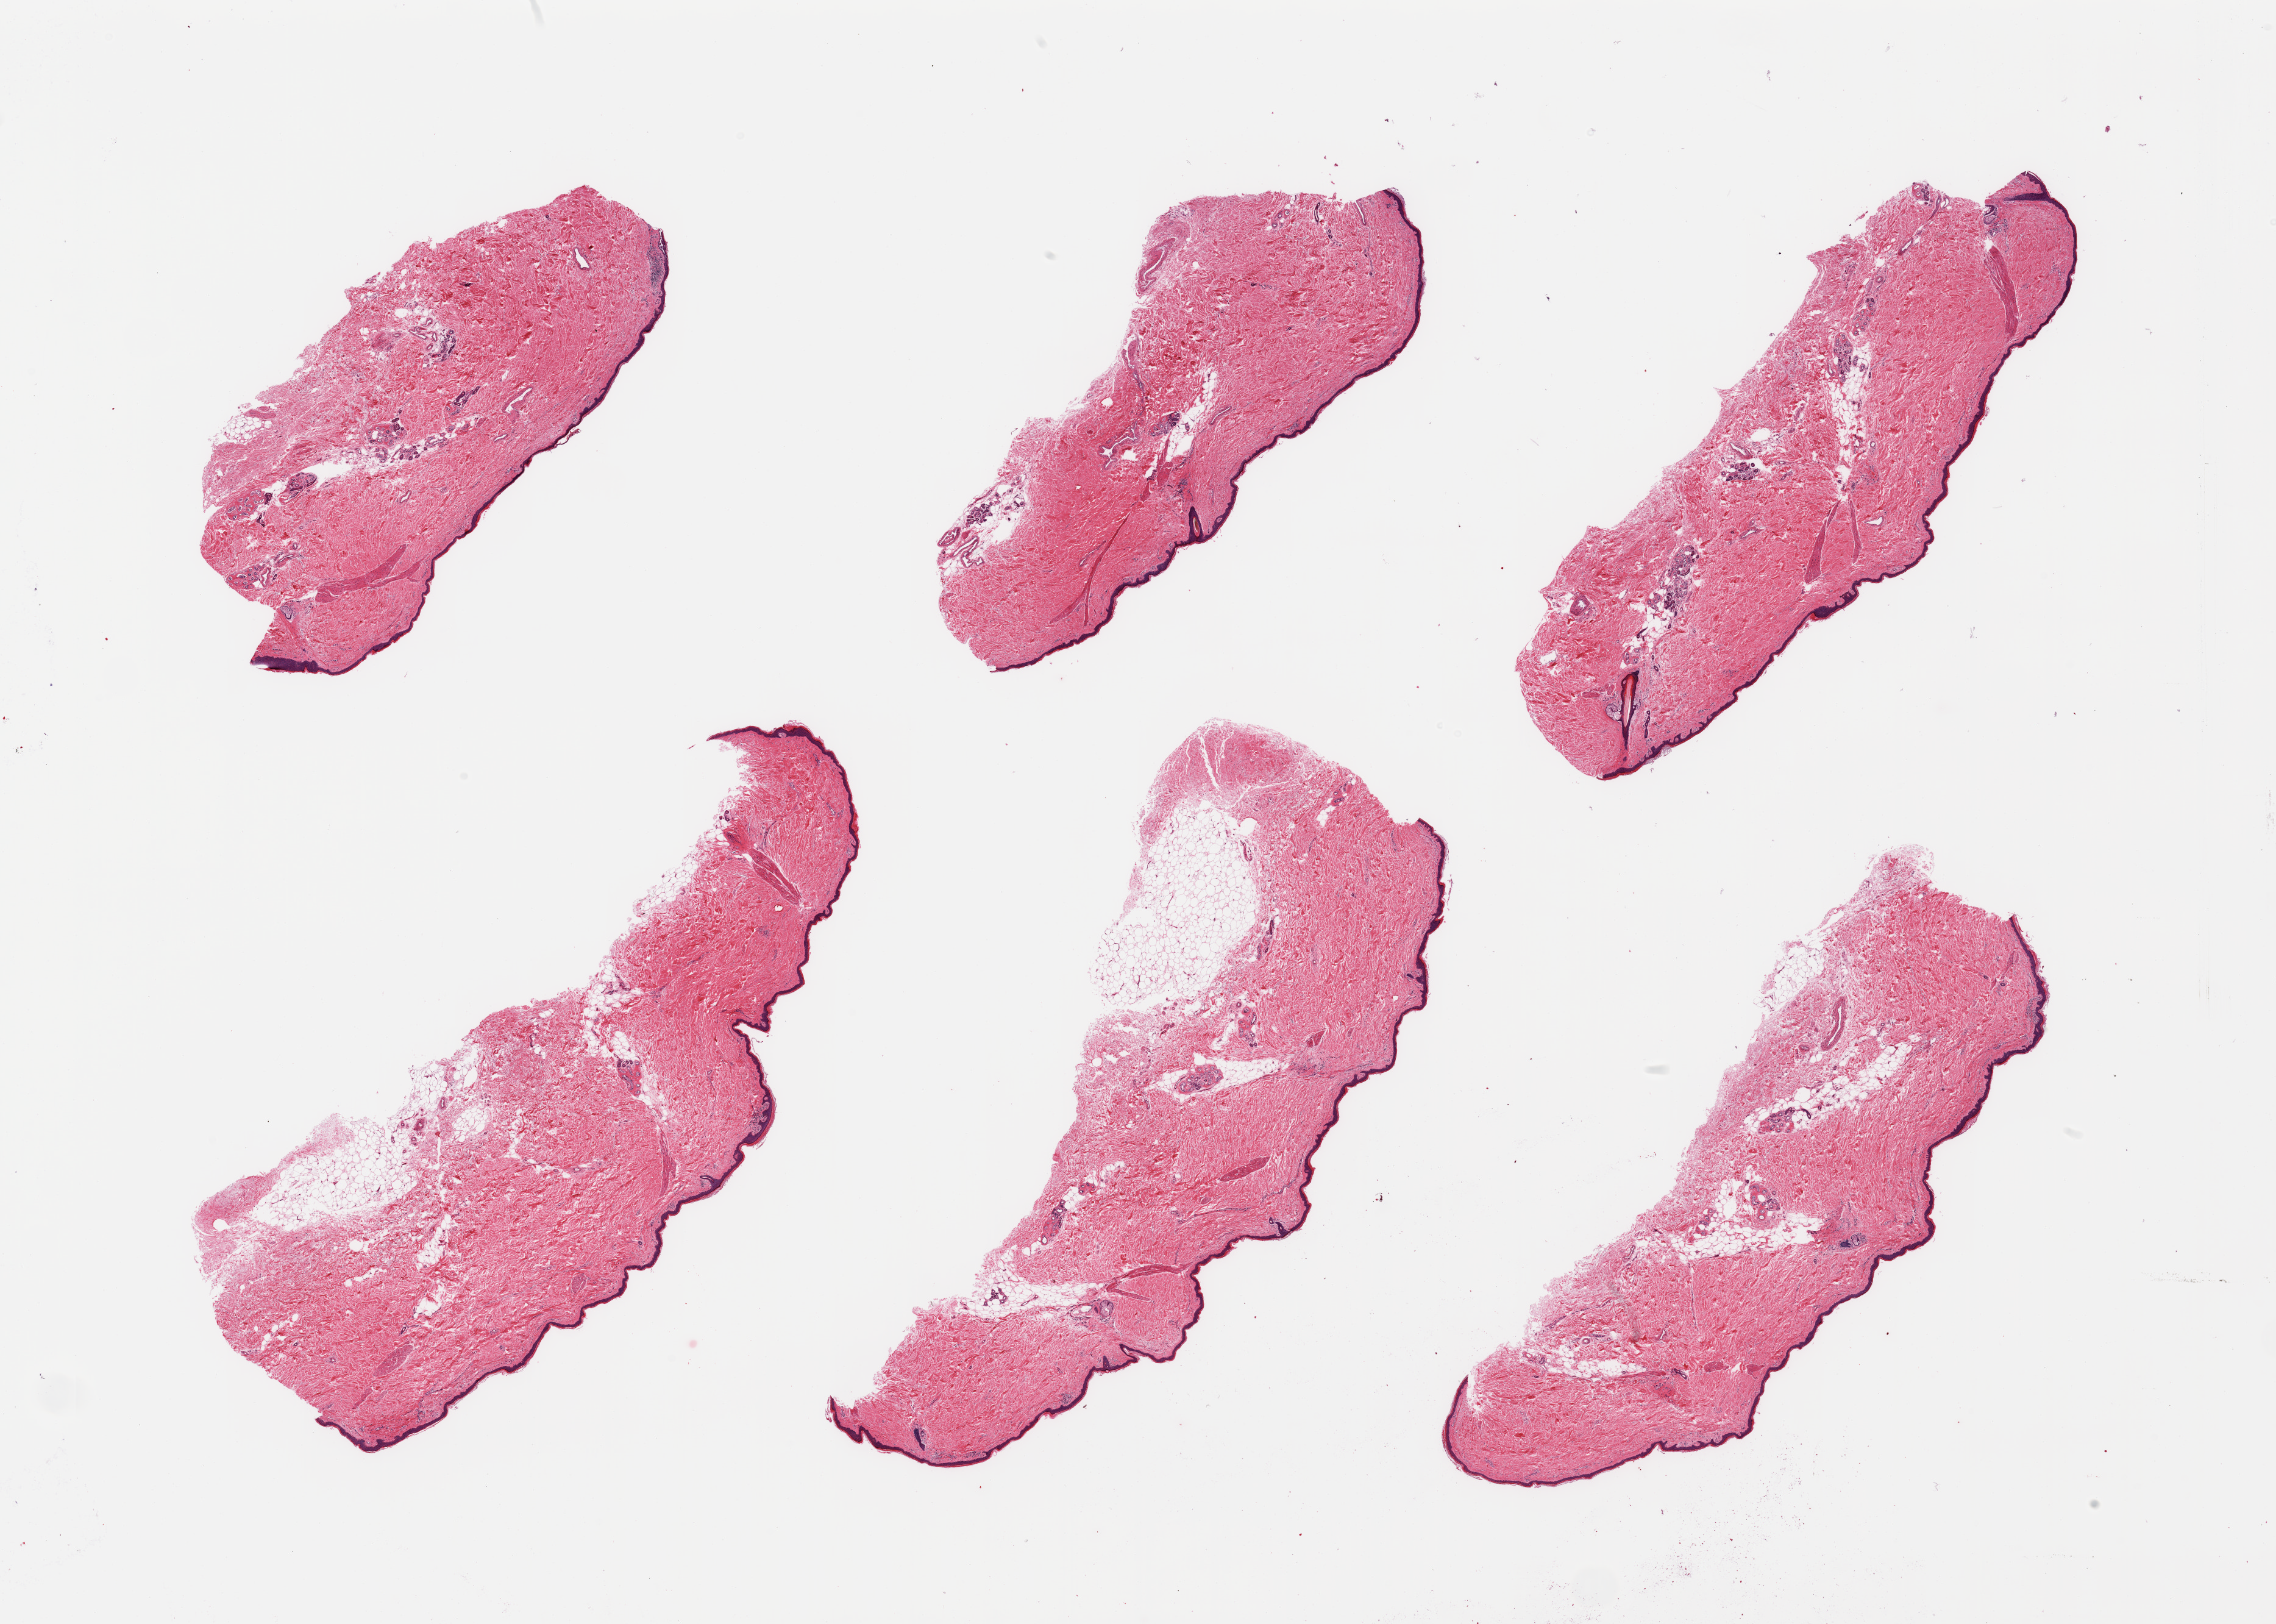
Whole-slide image, haematoxylin and eosin stain — a low-resolution overview of the entire scanned area, about 29.5 x 21.1 mm; PAXgene-fixed paraffin-embedded (PFPE) section; sampled site (target tissue): skin of lower leg; tissue donor sample. Male donor.
• review note (as recorded): 6 pieces; half well trimed; other 3 have up to 20% dermal fat